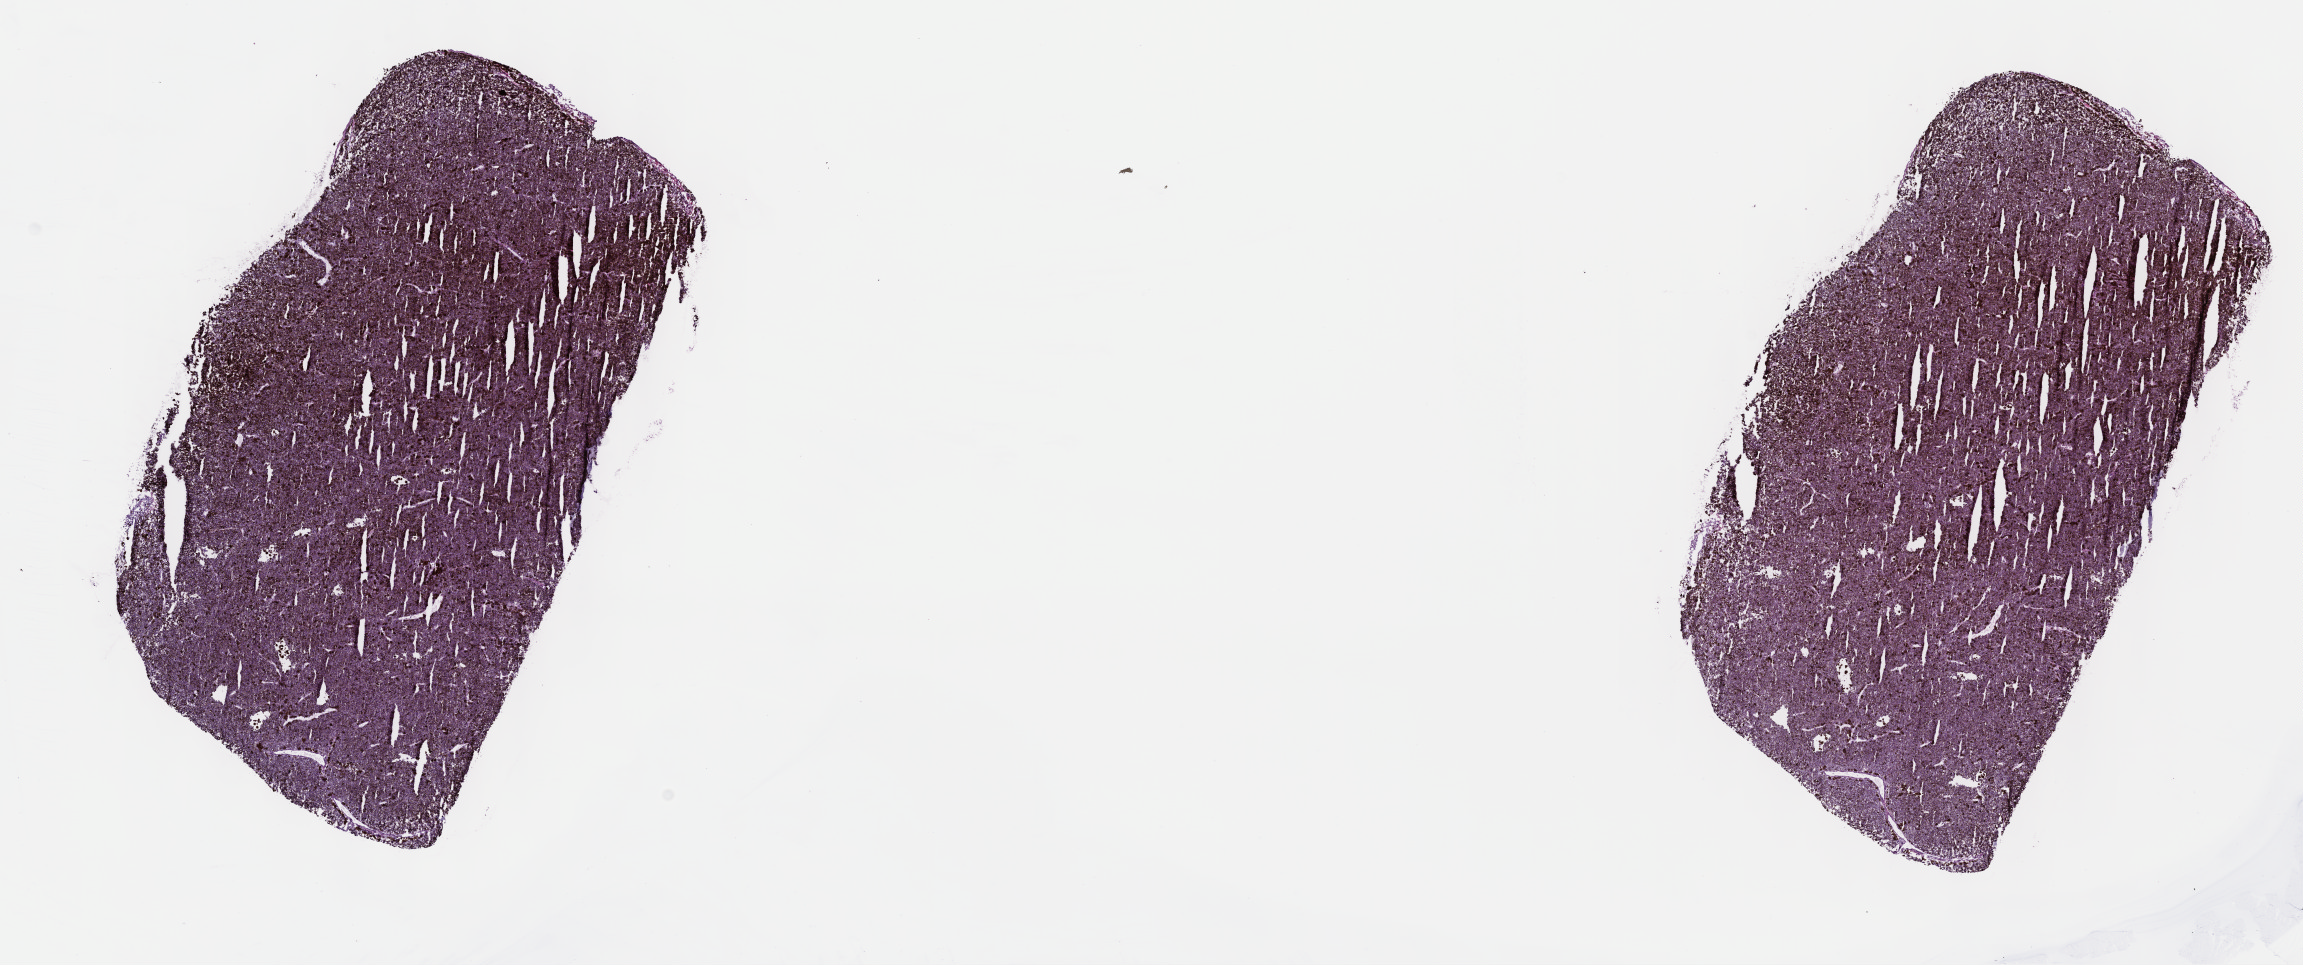
Digitized H&E tissue section (whole slide) — shown as a low-resolution overview of the whole scanned area (about 18.6 x 7.8 mm, from a 40x scan); frozen section; uvea, primary tumour sample. Patient: male, age at initial diagnosis 77 years. Pathologist review of this section (percent, as recorded): tumour cells 100%, tumour nuclei 80%.
Diagnosis: Mixed epithelioid and spindle cell melanoma (choroid).